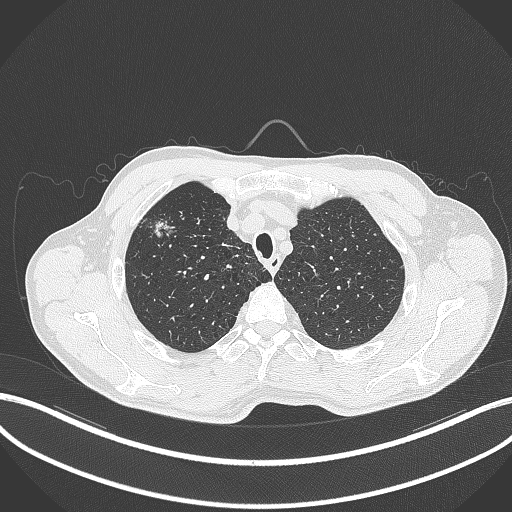
Chest CT, one axial slice; slice 351 of 427 in the series (ordered by position); reconstruction kernel B70f; lung window (W 1500 / L -600 HU); 1 mm slice thickness; 512 × 512 image matrix, field of view 400 × 400 mm. Male patient, age 69 years. Case-level facts recorded for this patient, not image findings: clinical TNM (as recorded): T1b N1 M0.
Outlined on this slice (rectangle marked by the reading radiologist):
- lung tumour (recorded histology: adenocarcinoma): box from (x=143, y=214) to (x=179, y=243) px